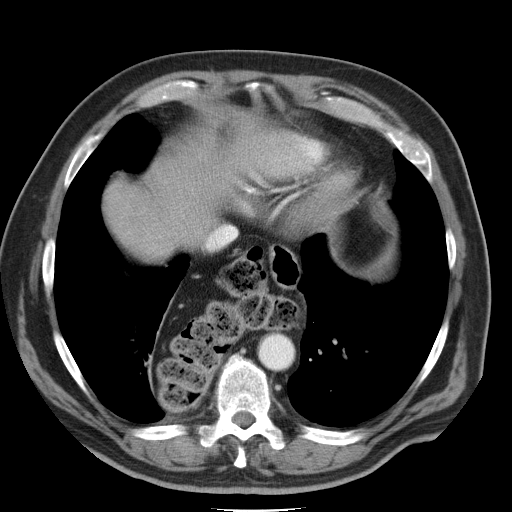
Contrast-enhanced abdominal CT, one axial slice. Slice 41 of 45 in the series (ordered by position). 120 kVp. Intravenous contrast given. Soft-tissue window (W 400 / L 40 HU). 512 × 512 image matrix, field of view 386 × 386 mm. Male patient, age 65 years. From the clinical record (not read from this slice): diagnosis: colorectal cancer liver metastases, imaged before liver resection; multiple liver metastases: yes; largest metastasis: 4.9 cm; chemotherapy before resection: yes.
Structures marked on this image (outlined manually by an expert reader):
- hepatic veins: bounding box <207,226,227,248> (left, top, right, bottom; pixels)
- liver: <108,153,223,257>
- planned liver remnant (the part of the liver to remain after resection): <151,154,223,237>